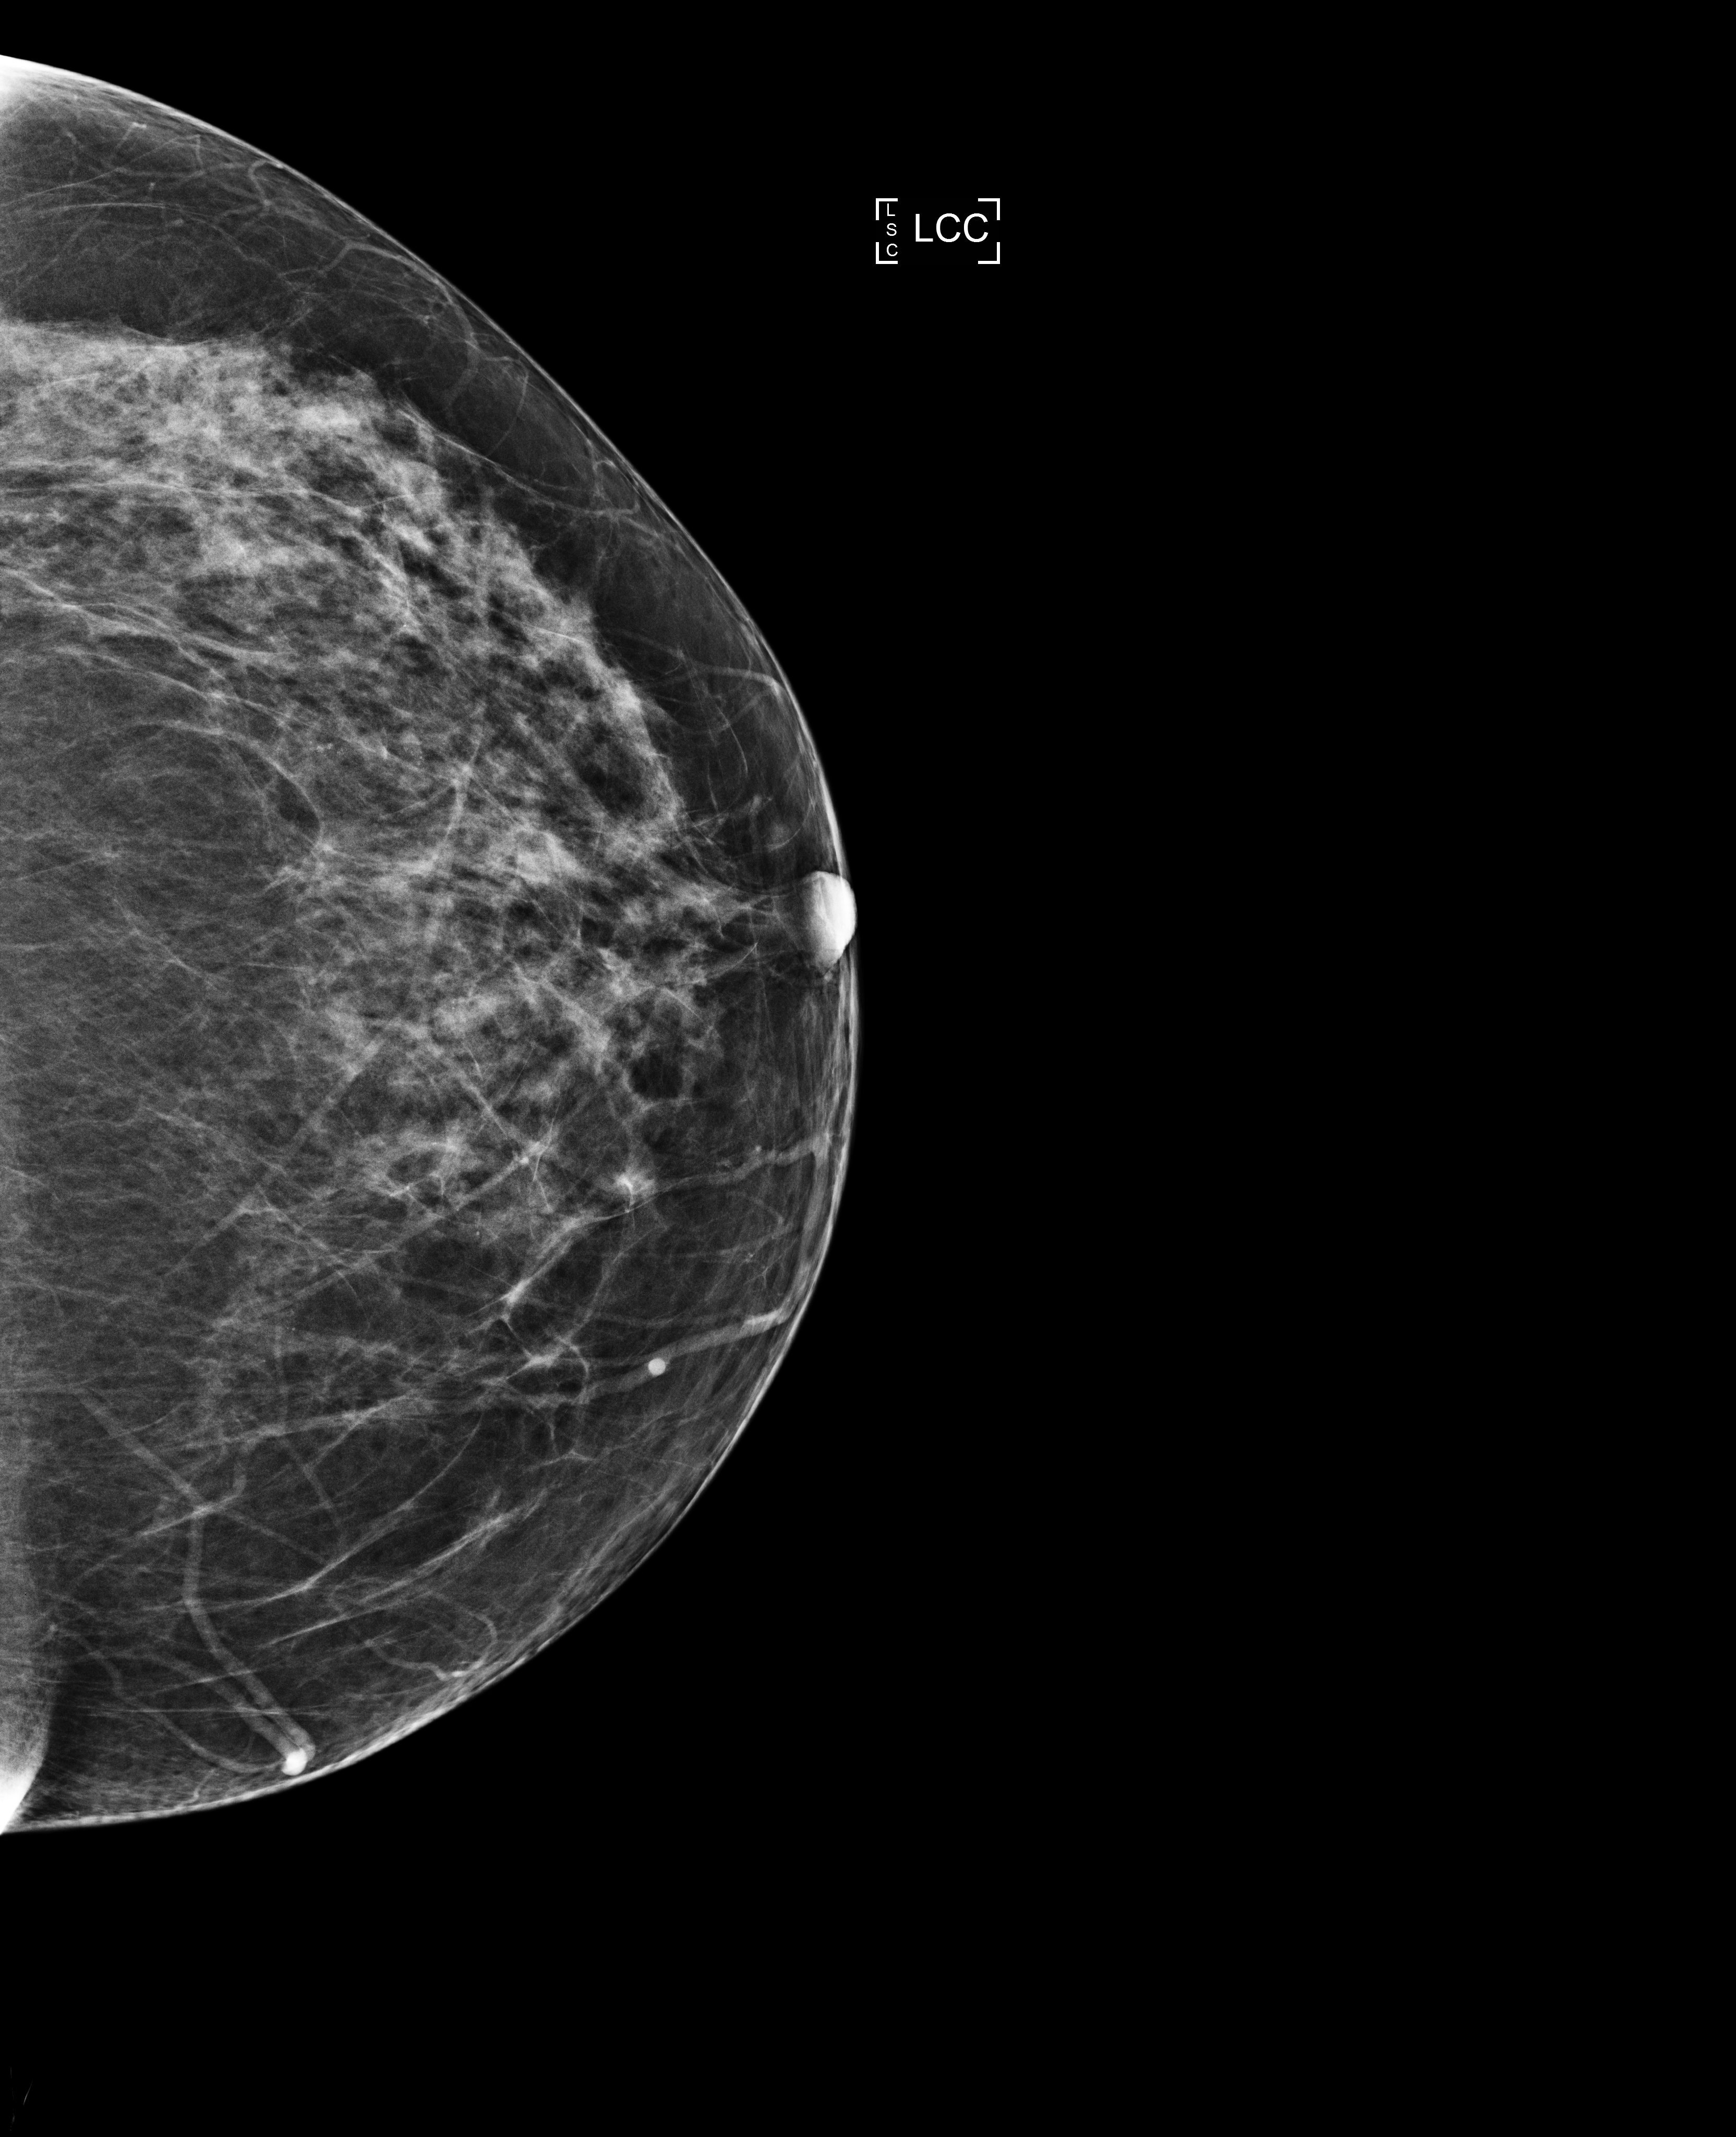
Full-field digital mammogram (FFDM), left breast, cranio-caudal projection, screening examination. Female patient, age 57 years.
- breast density at the screening exam (both breasts): heterogeneously dense (BI-RADS density category c)
- final BI-RADS category for the screening round (tomosynthesis exam, both breasts): category 2
- recall: no recall after this screen